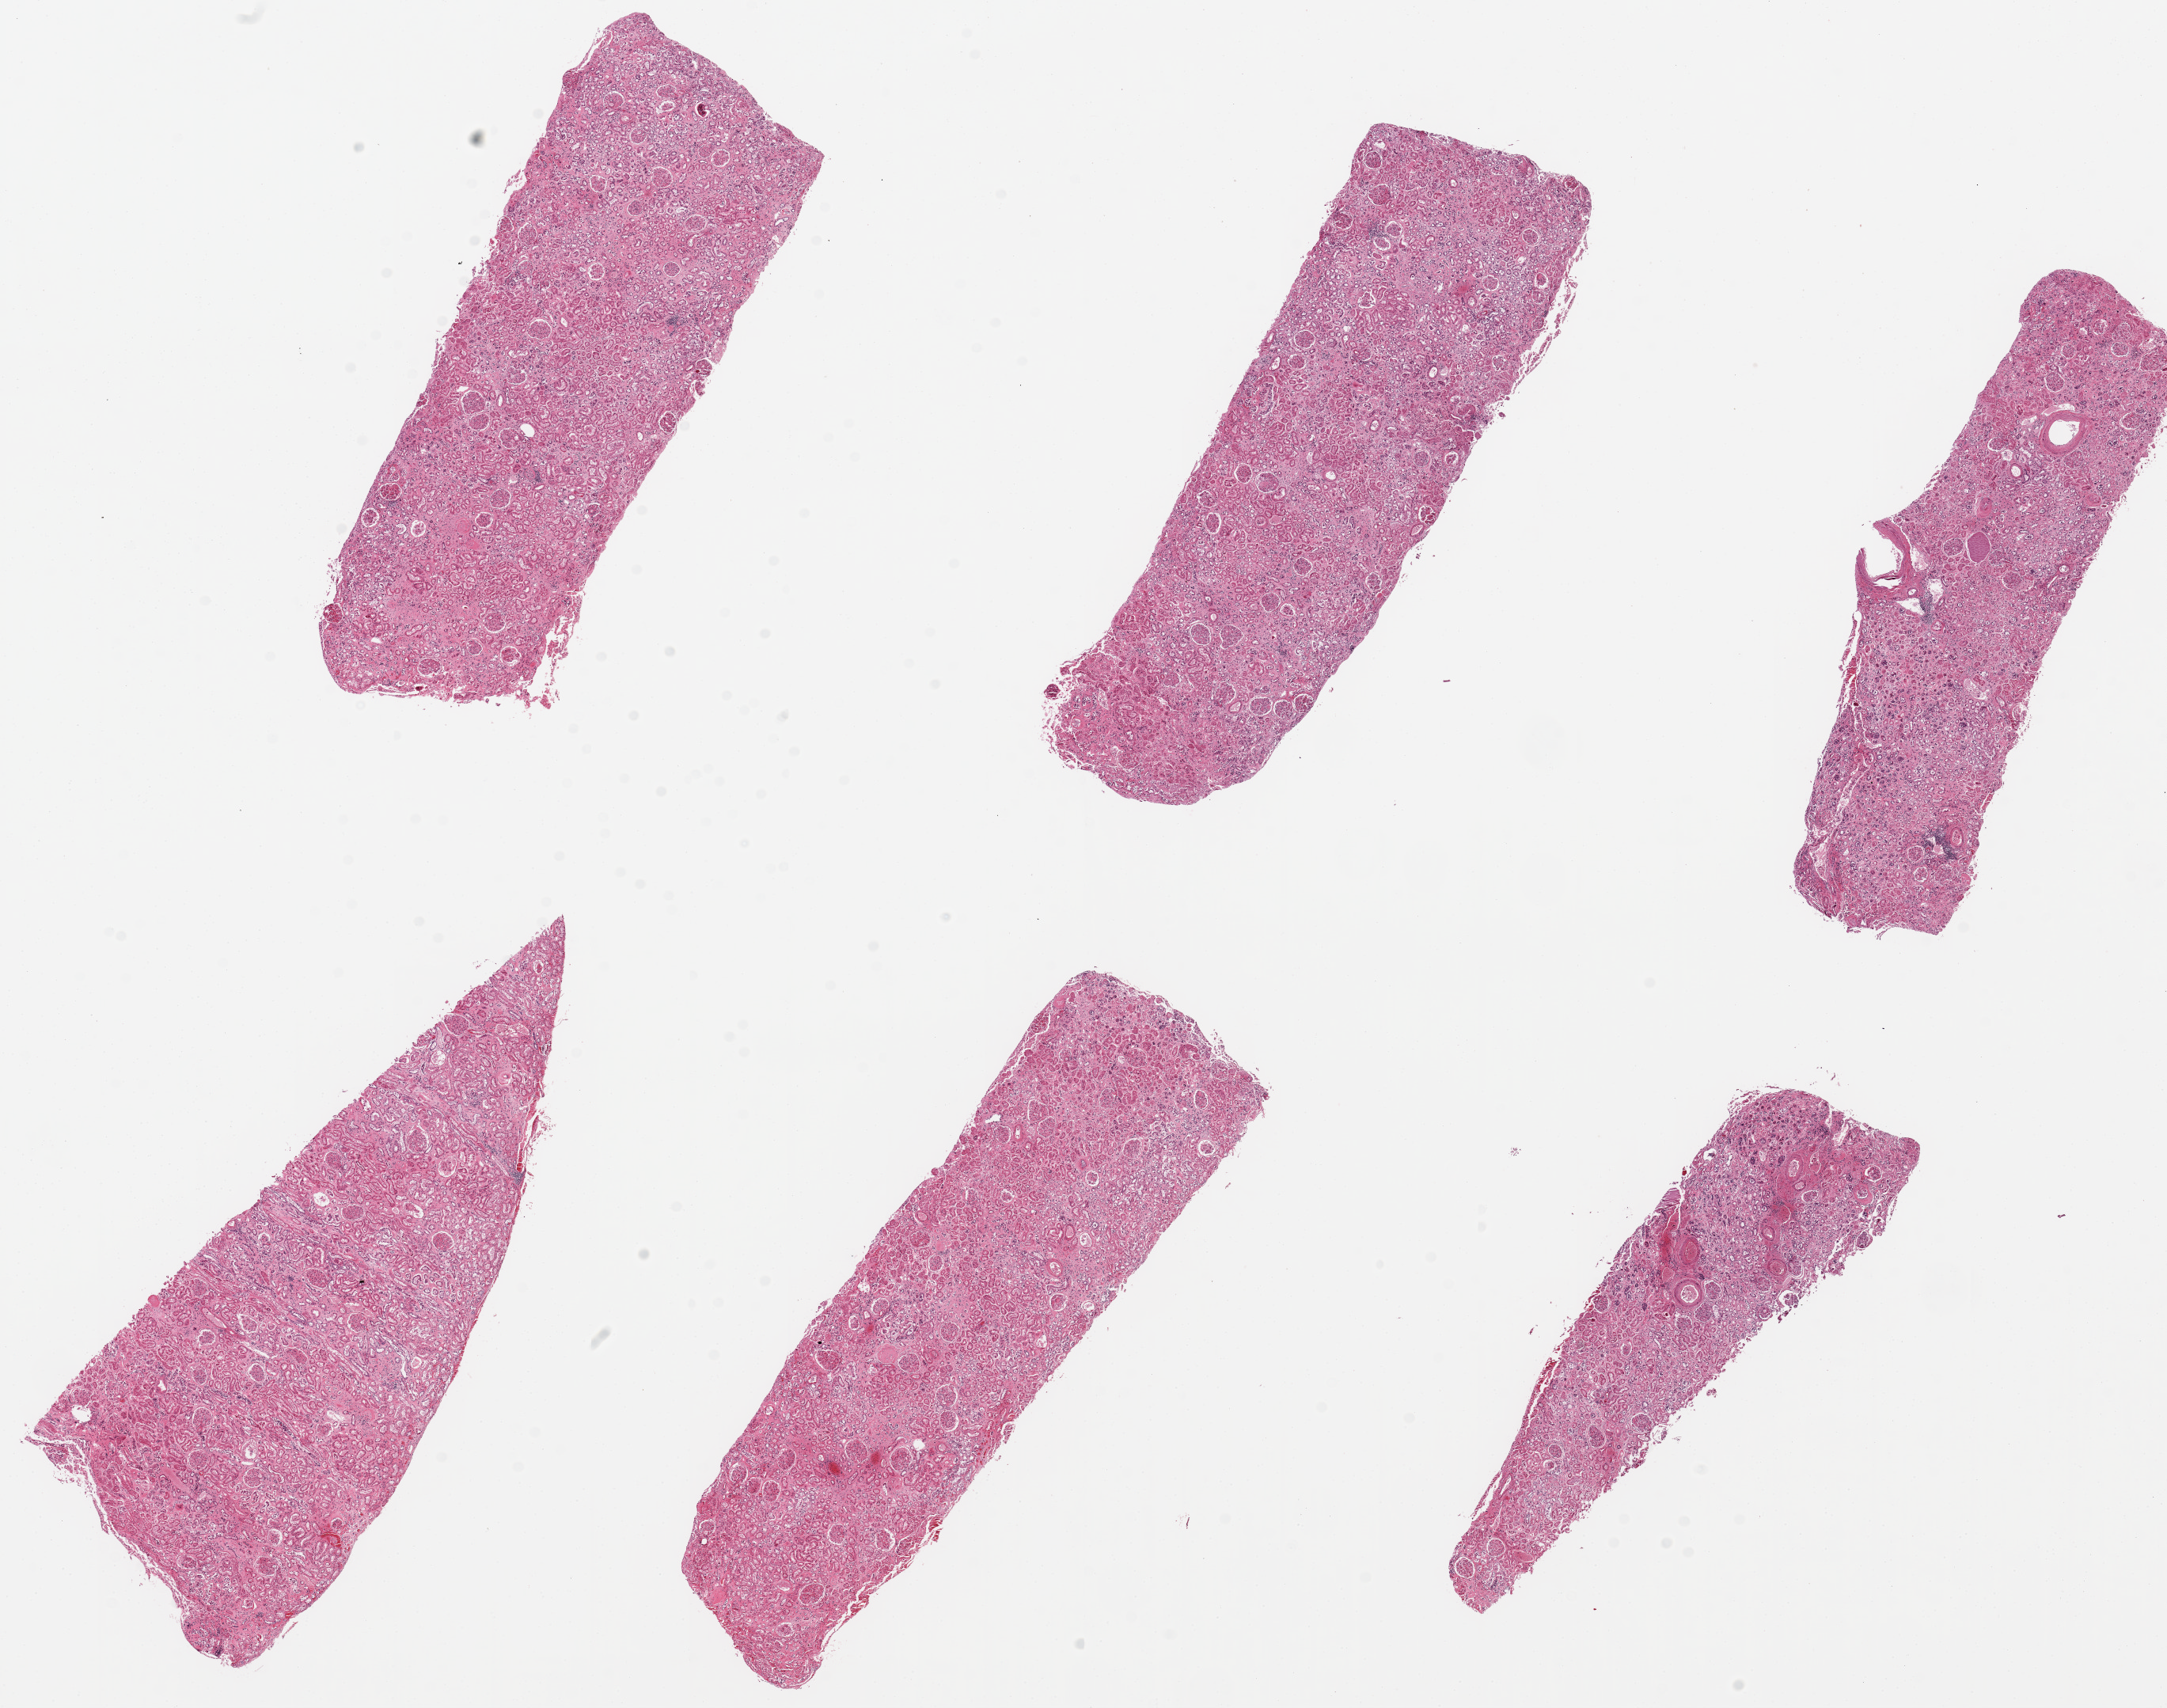
Hematoxylin and eosin (H&E) whole-slide image, brightfield, whole scanned area (about 21.7 x 17.1 mm, slide scanned at 20x) shown as a low-resolution overview, PAXgene-fixed paraffin-embedded (PFPE) section, section of renal cortex (target tissue), donor tissue sample.
Review note (as recorded): 6 pieces, up to 8x2mm; all are cortex; moderate glomerular and arteriolar sclerosis.